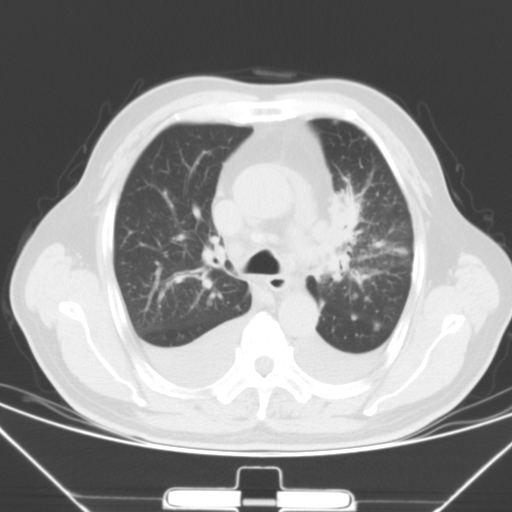
Chest CT, one axial slice. 120 kVp. Lung window (W 1500 / L -600 HU). 5 mm slice thickness. 512 × 512 image matrix, field of view 352 × 352 mm. Male patient, age 66 years. Case-level facts recorded for this patient, not image findings: clinical TNM (as recorded): T1c N0 M0.
Outlined on this slice (rectangle marked by the reading radiologist):
- lung tumour (recorded histology: adenocarcinoma): bounding box (x1, y1, x2, y2) in pixels: (327, 189, 363, 248)